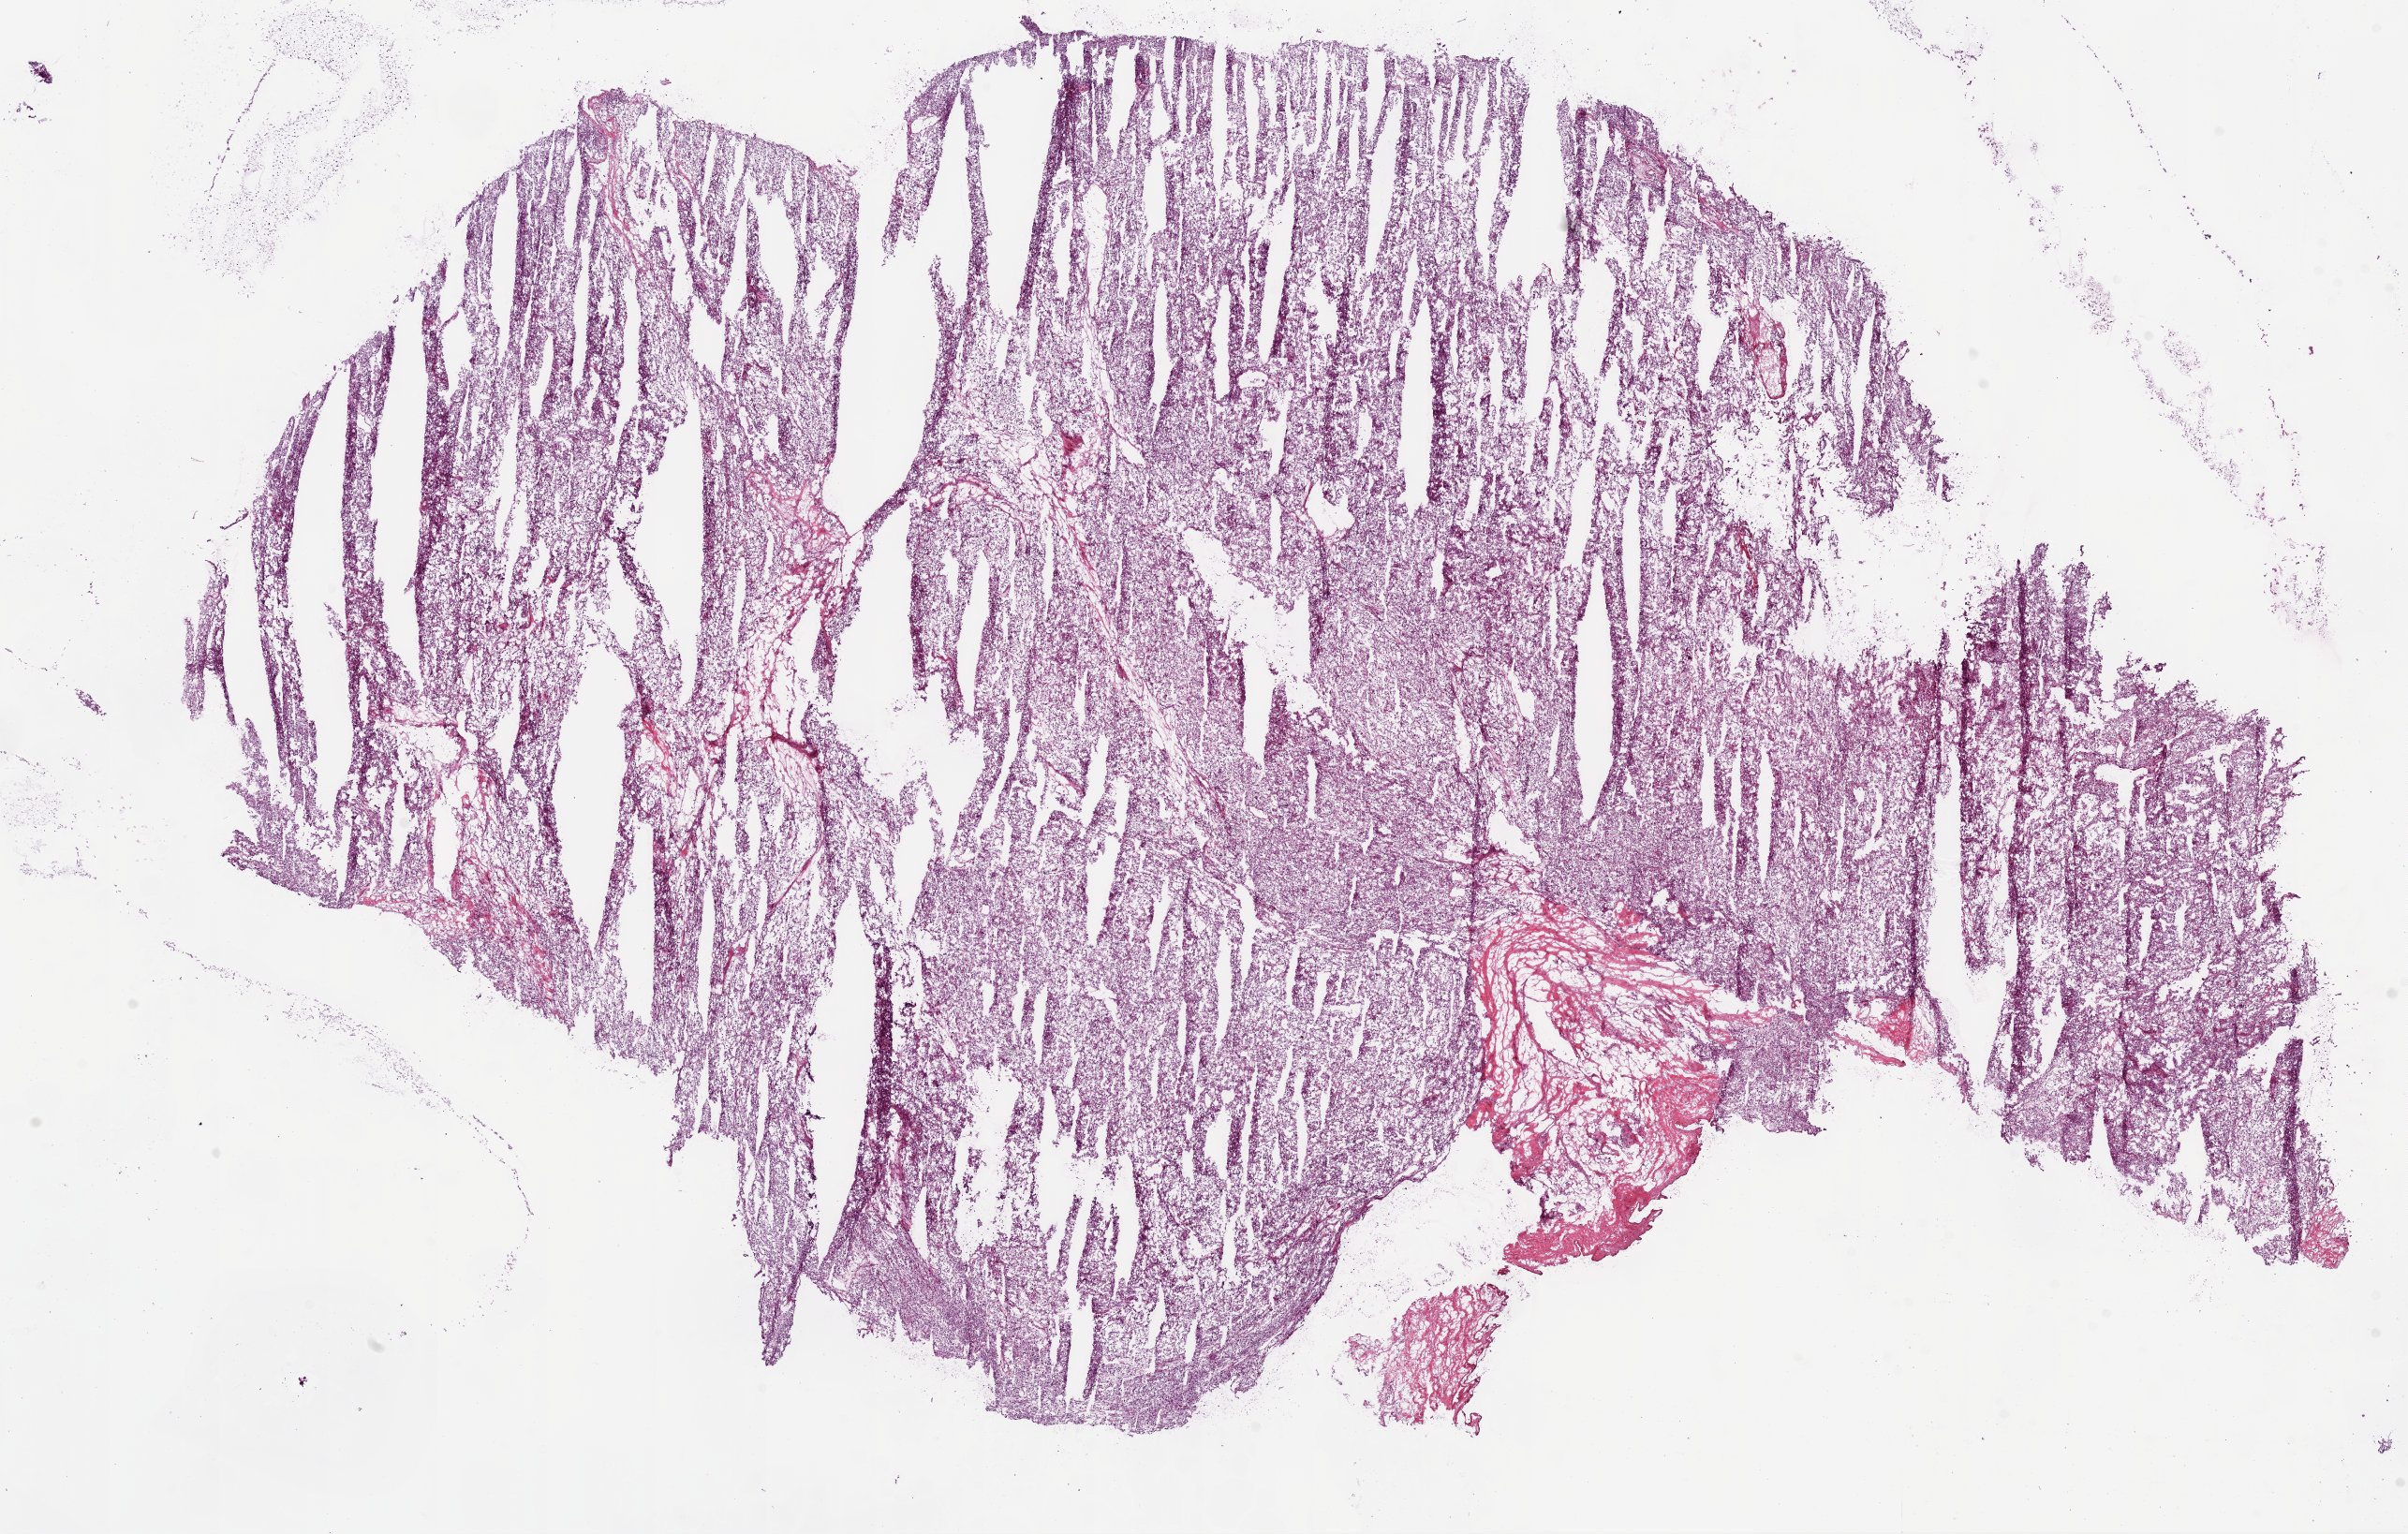
H&E whole-slide image — low-resolution overview of the scanned area, about 20.6 x 13.1 mm; frozen section; primary tumour sample from the kidney. Patient: male, age at initial diagnosis 64 years. Histologic grade: G4 (undifferentiated). Composition of this section per pathologist review: tumour cells 95%, tumour nuclei 85%, normal cells 0%, stromal cells 5%, necrosis 0%.
• histologic diagnosis: Clear cell adenocarcinoma, NOS
• laterality: left
• AJCC pathologic stage: IV